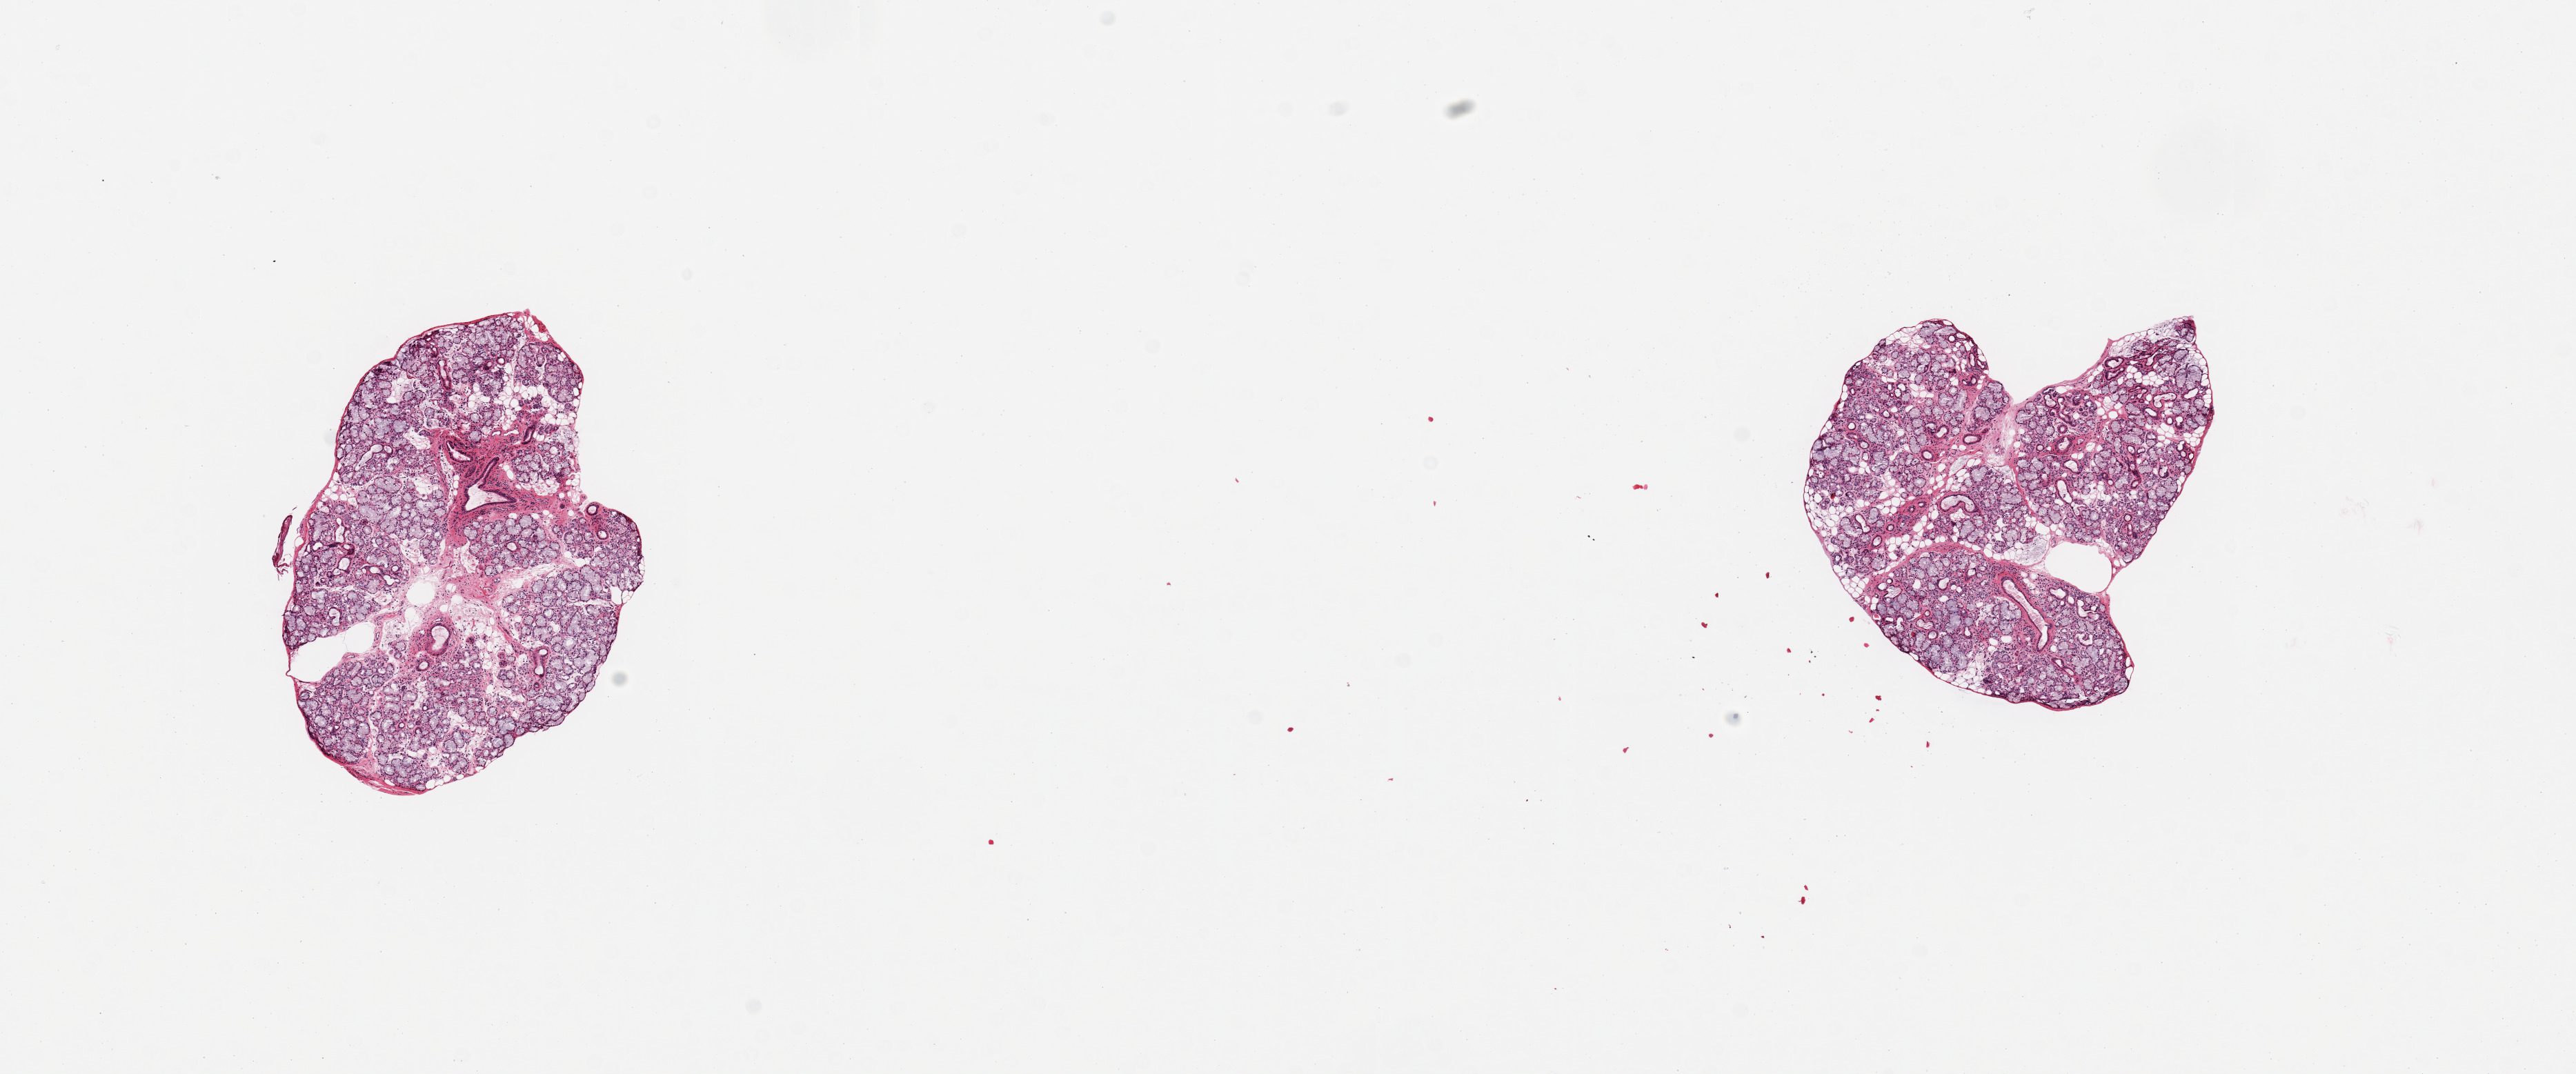
Hematoxylin and eosin (H&E) whole-slide image, shown as a low-resolution overview of the whole scanned area (about 14.8 x 6.2 mm). PAXgene-fixed, paraffin-embedded tissue. Sampled site (target tissue): minor salivary gland. Tissue donor sample. Donor sex: female.
Pathologist's review note for this sample: 2 pieces; very well dissected glands.